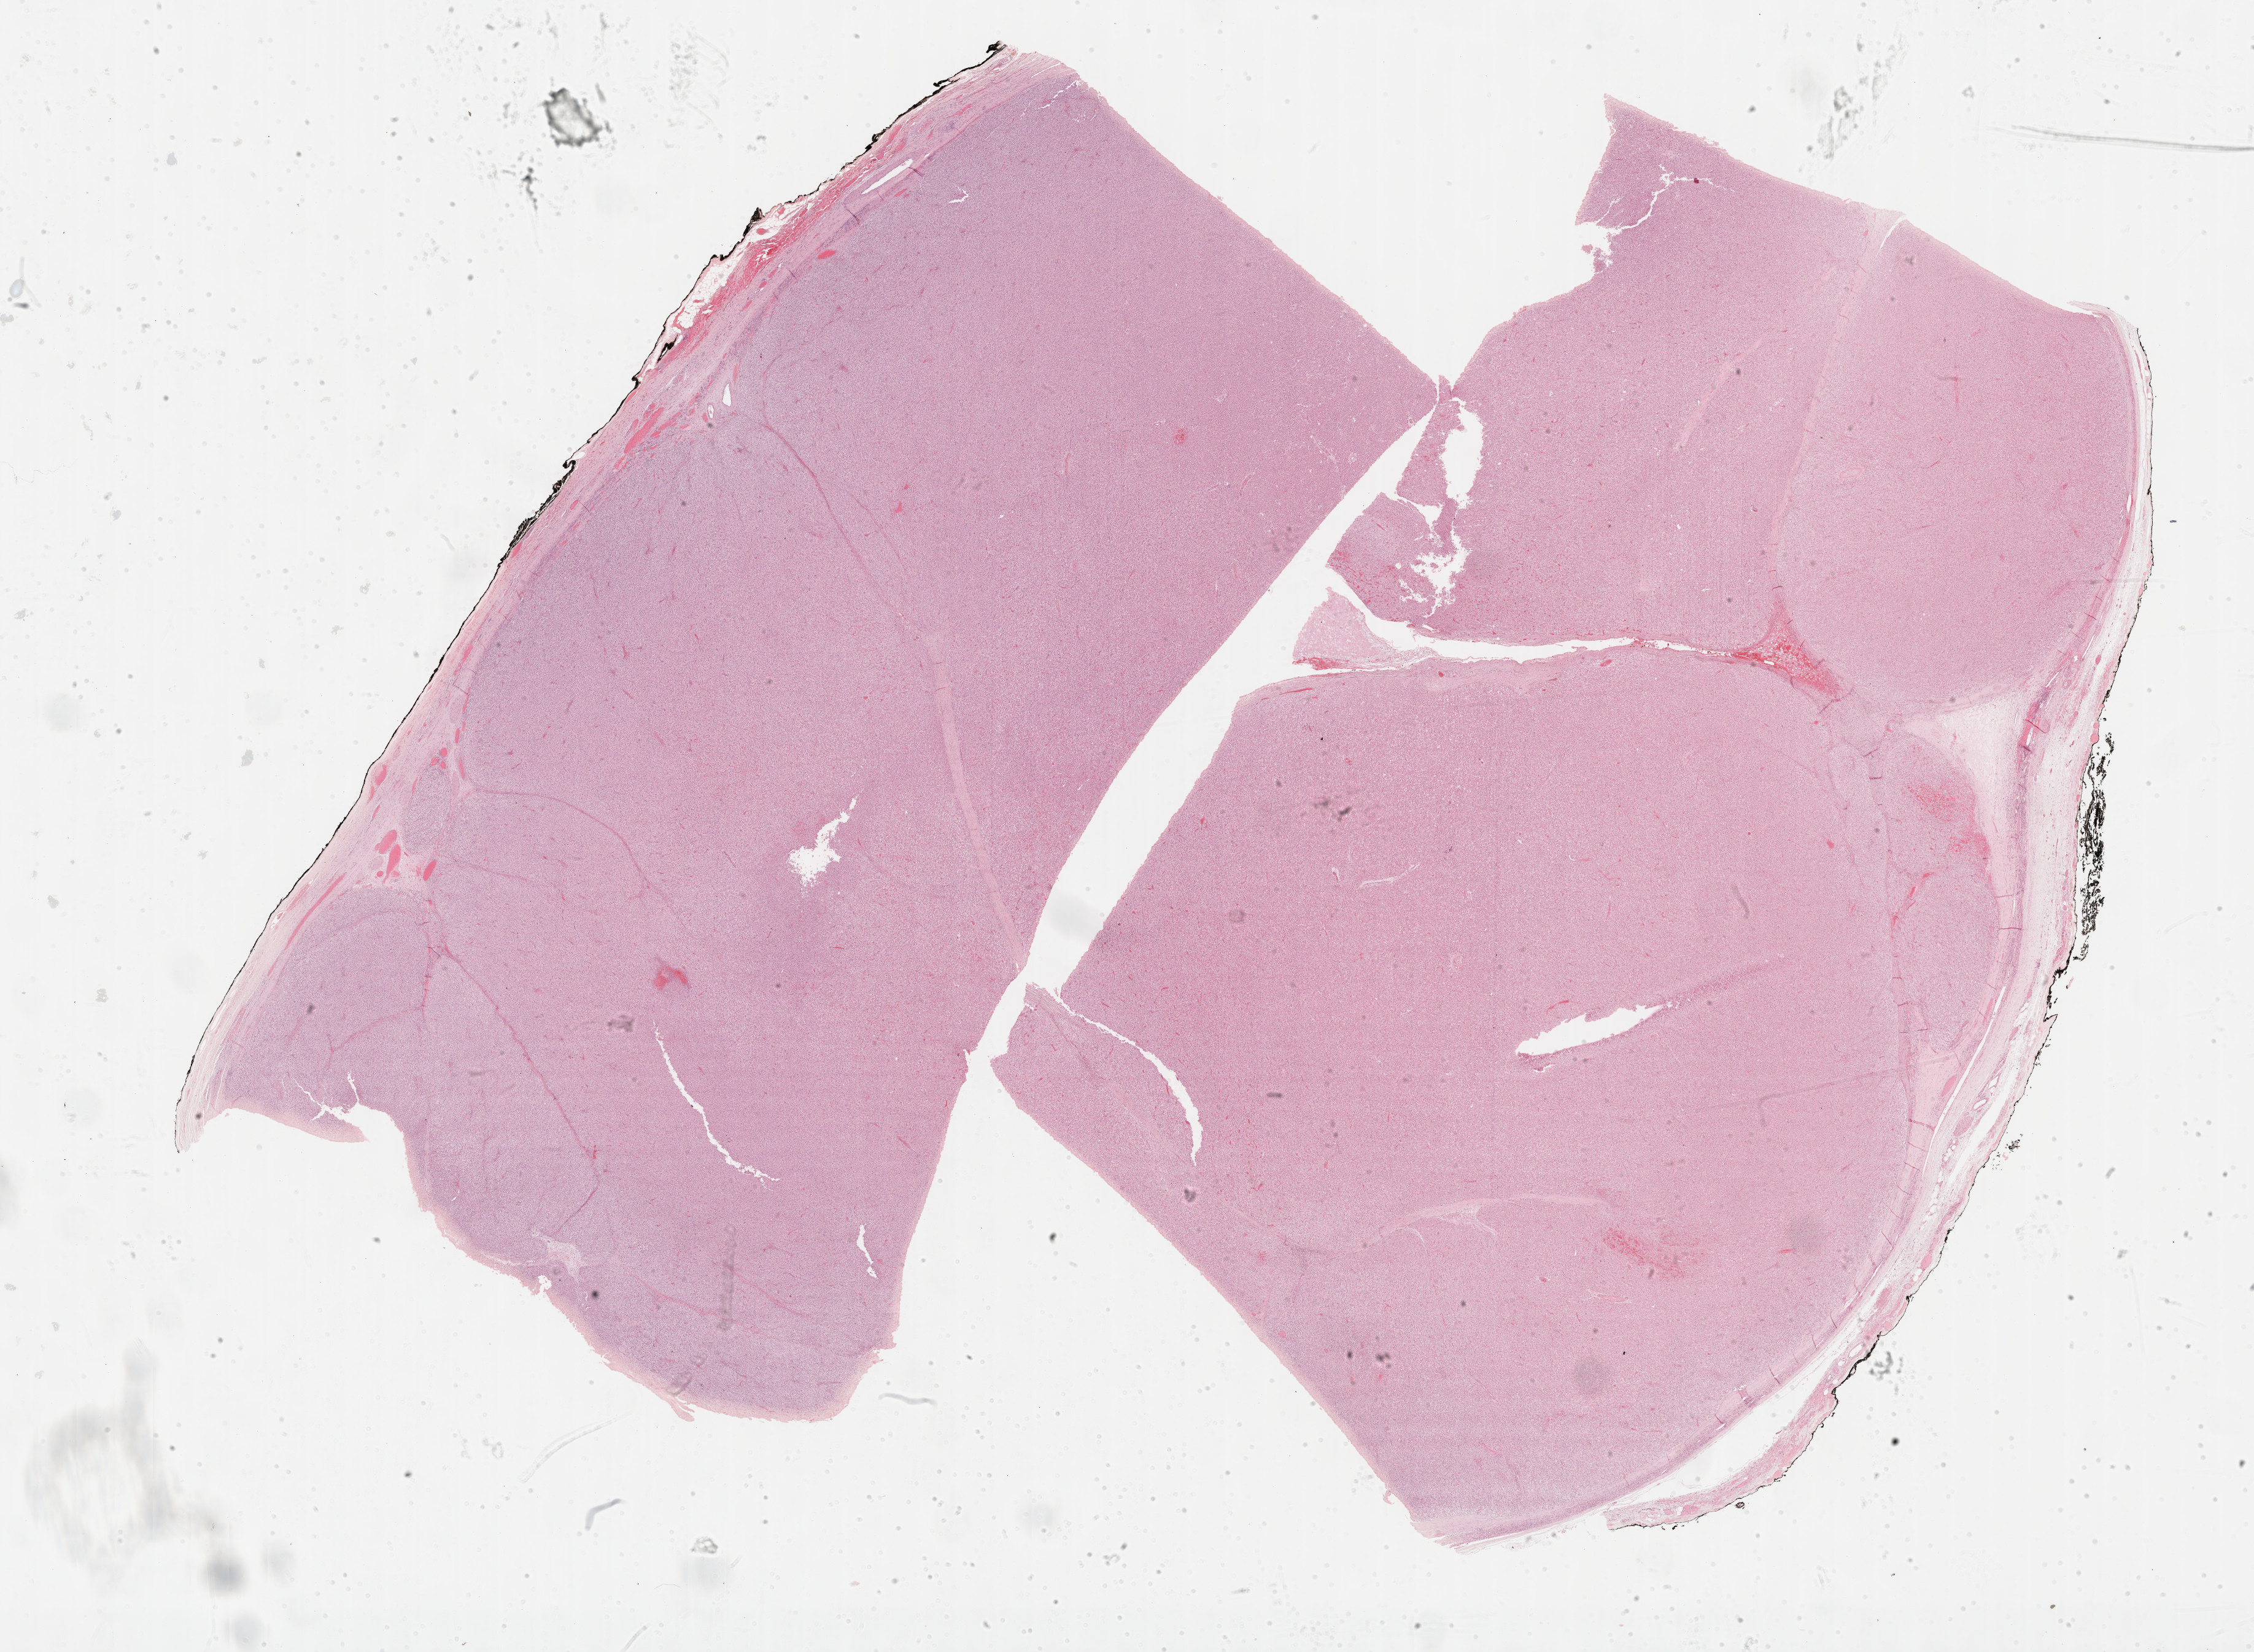
H&E whole-slide image, shown as a low-resolution overview of the whole scanned area (about 29.7 x 21.8 mm, from a 40x scan); formalin-fixed paraffin-embedded (FFPE) diagnostic section; sample: primary tumour, adrenal cortex. Male patient; age at initial diagnosis 48 years.
Diagnosis: Adrenal cortical carcinoma.